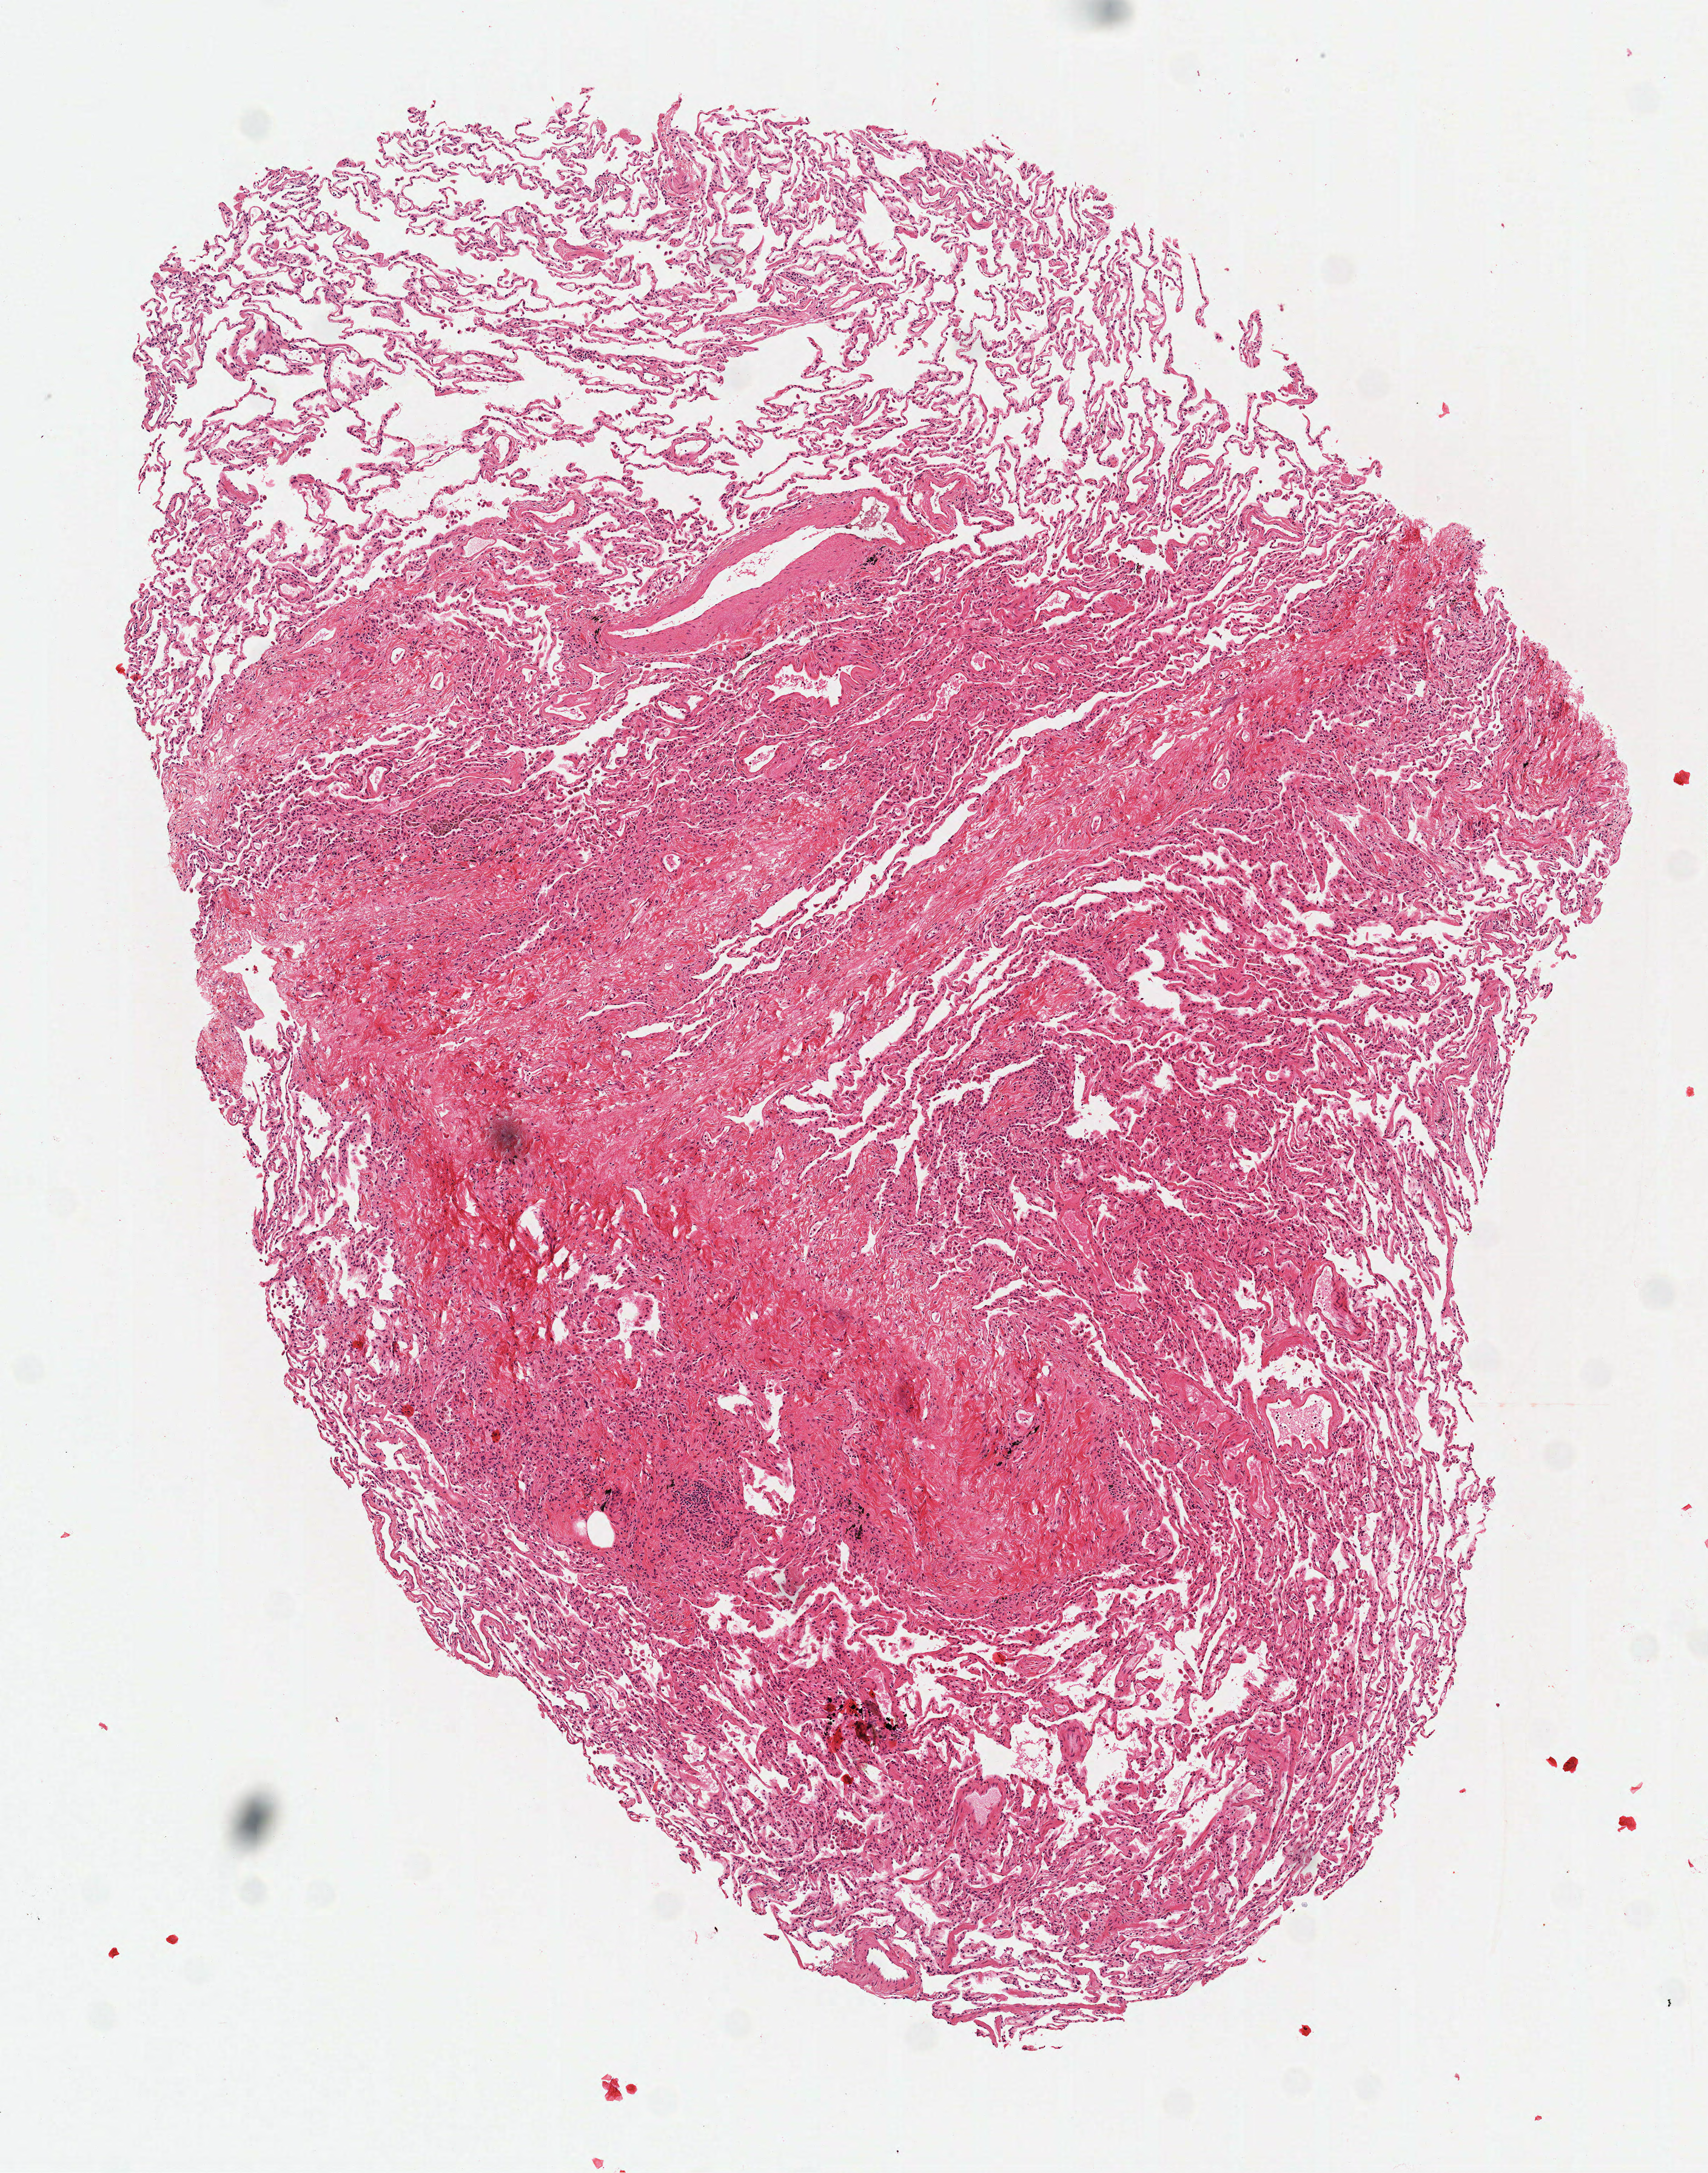
Whole-slide histology image, H&E-stained, whole scanned area (about 4.8 x 6.1 mm, slide scanned at 40x) shown as a low-resolution overview. Frozen section. Solid tissue normal (non-tumour tissue) sample from the lung. Patient: male, age at initial diagnosis 56 years.
This section: solid tissue normal (non-tumour) sample from the same patient. Patient diagnosis: Squamous cell carcinoma, NOS.